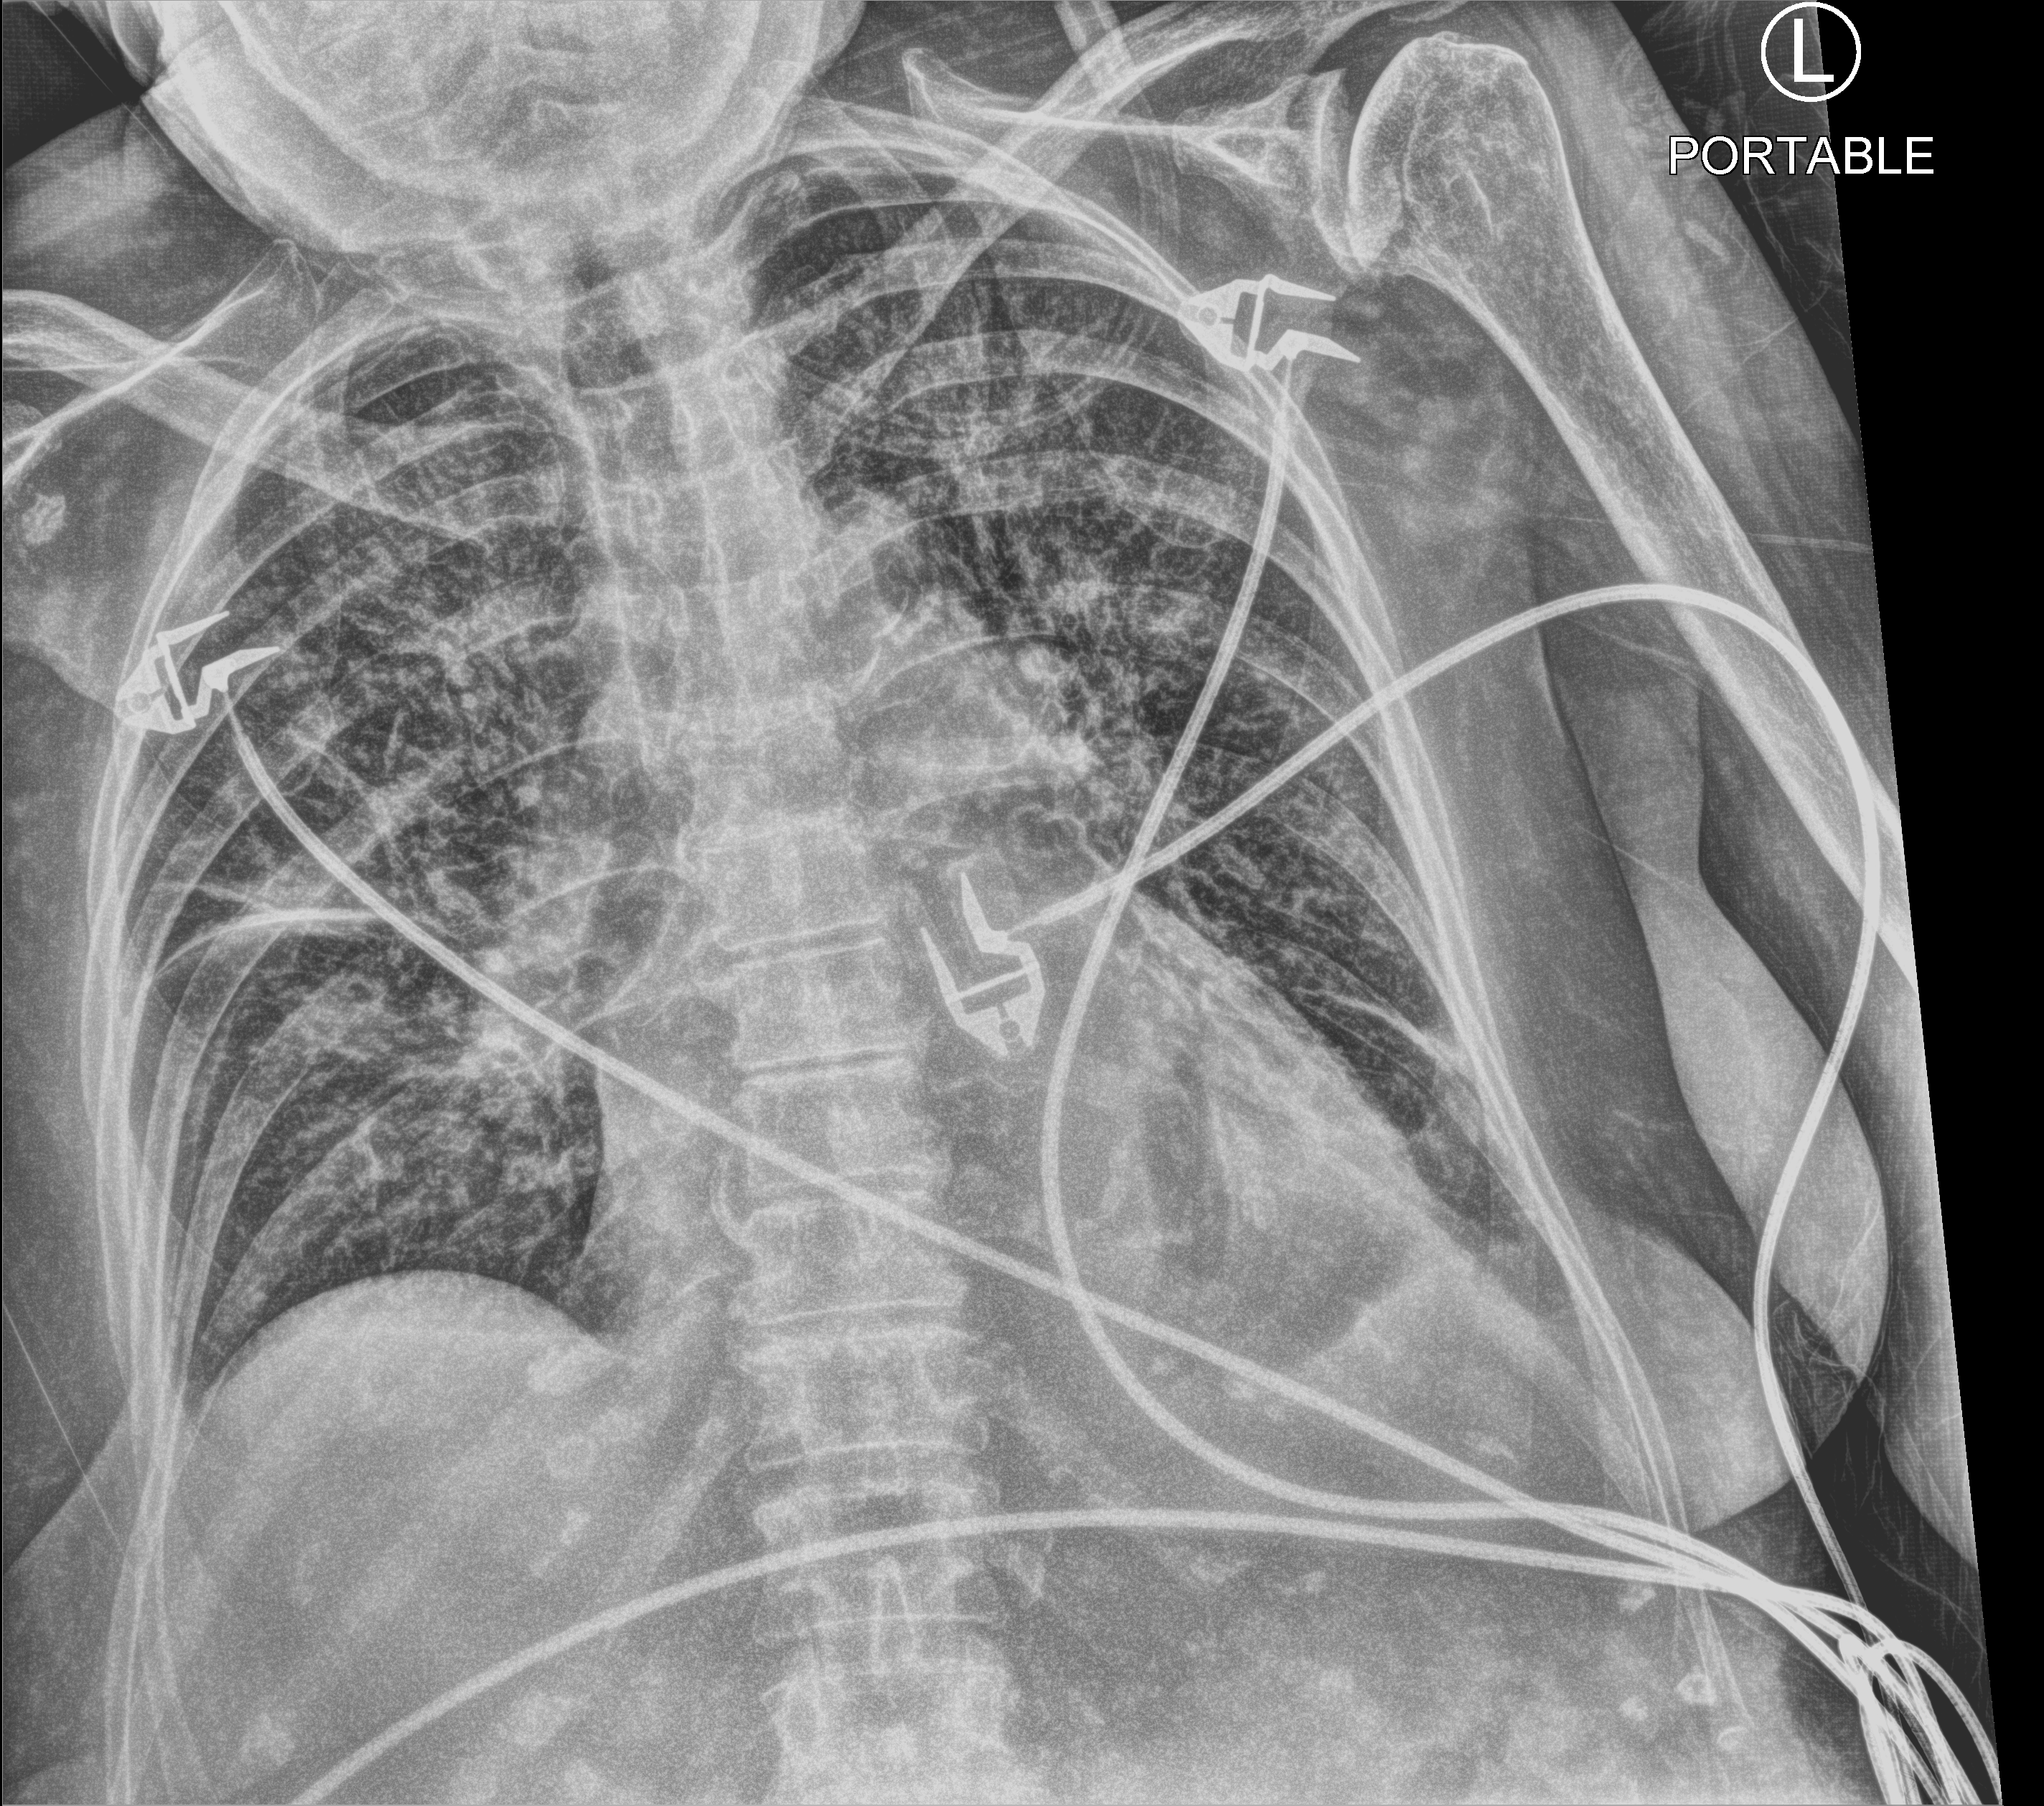
Portable chest radiograph; anteroposterior (AP) projection. Female patient hospitalised with COVID-19, age 75–90 years.
Admission-level facts for this patient (not findings on this image; timing relative to this image not recorded): mechanically ventilated during this hospital stay: no.